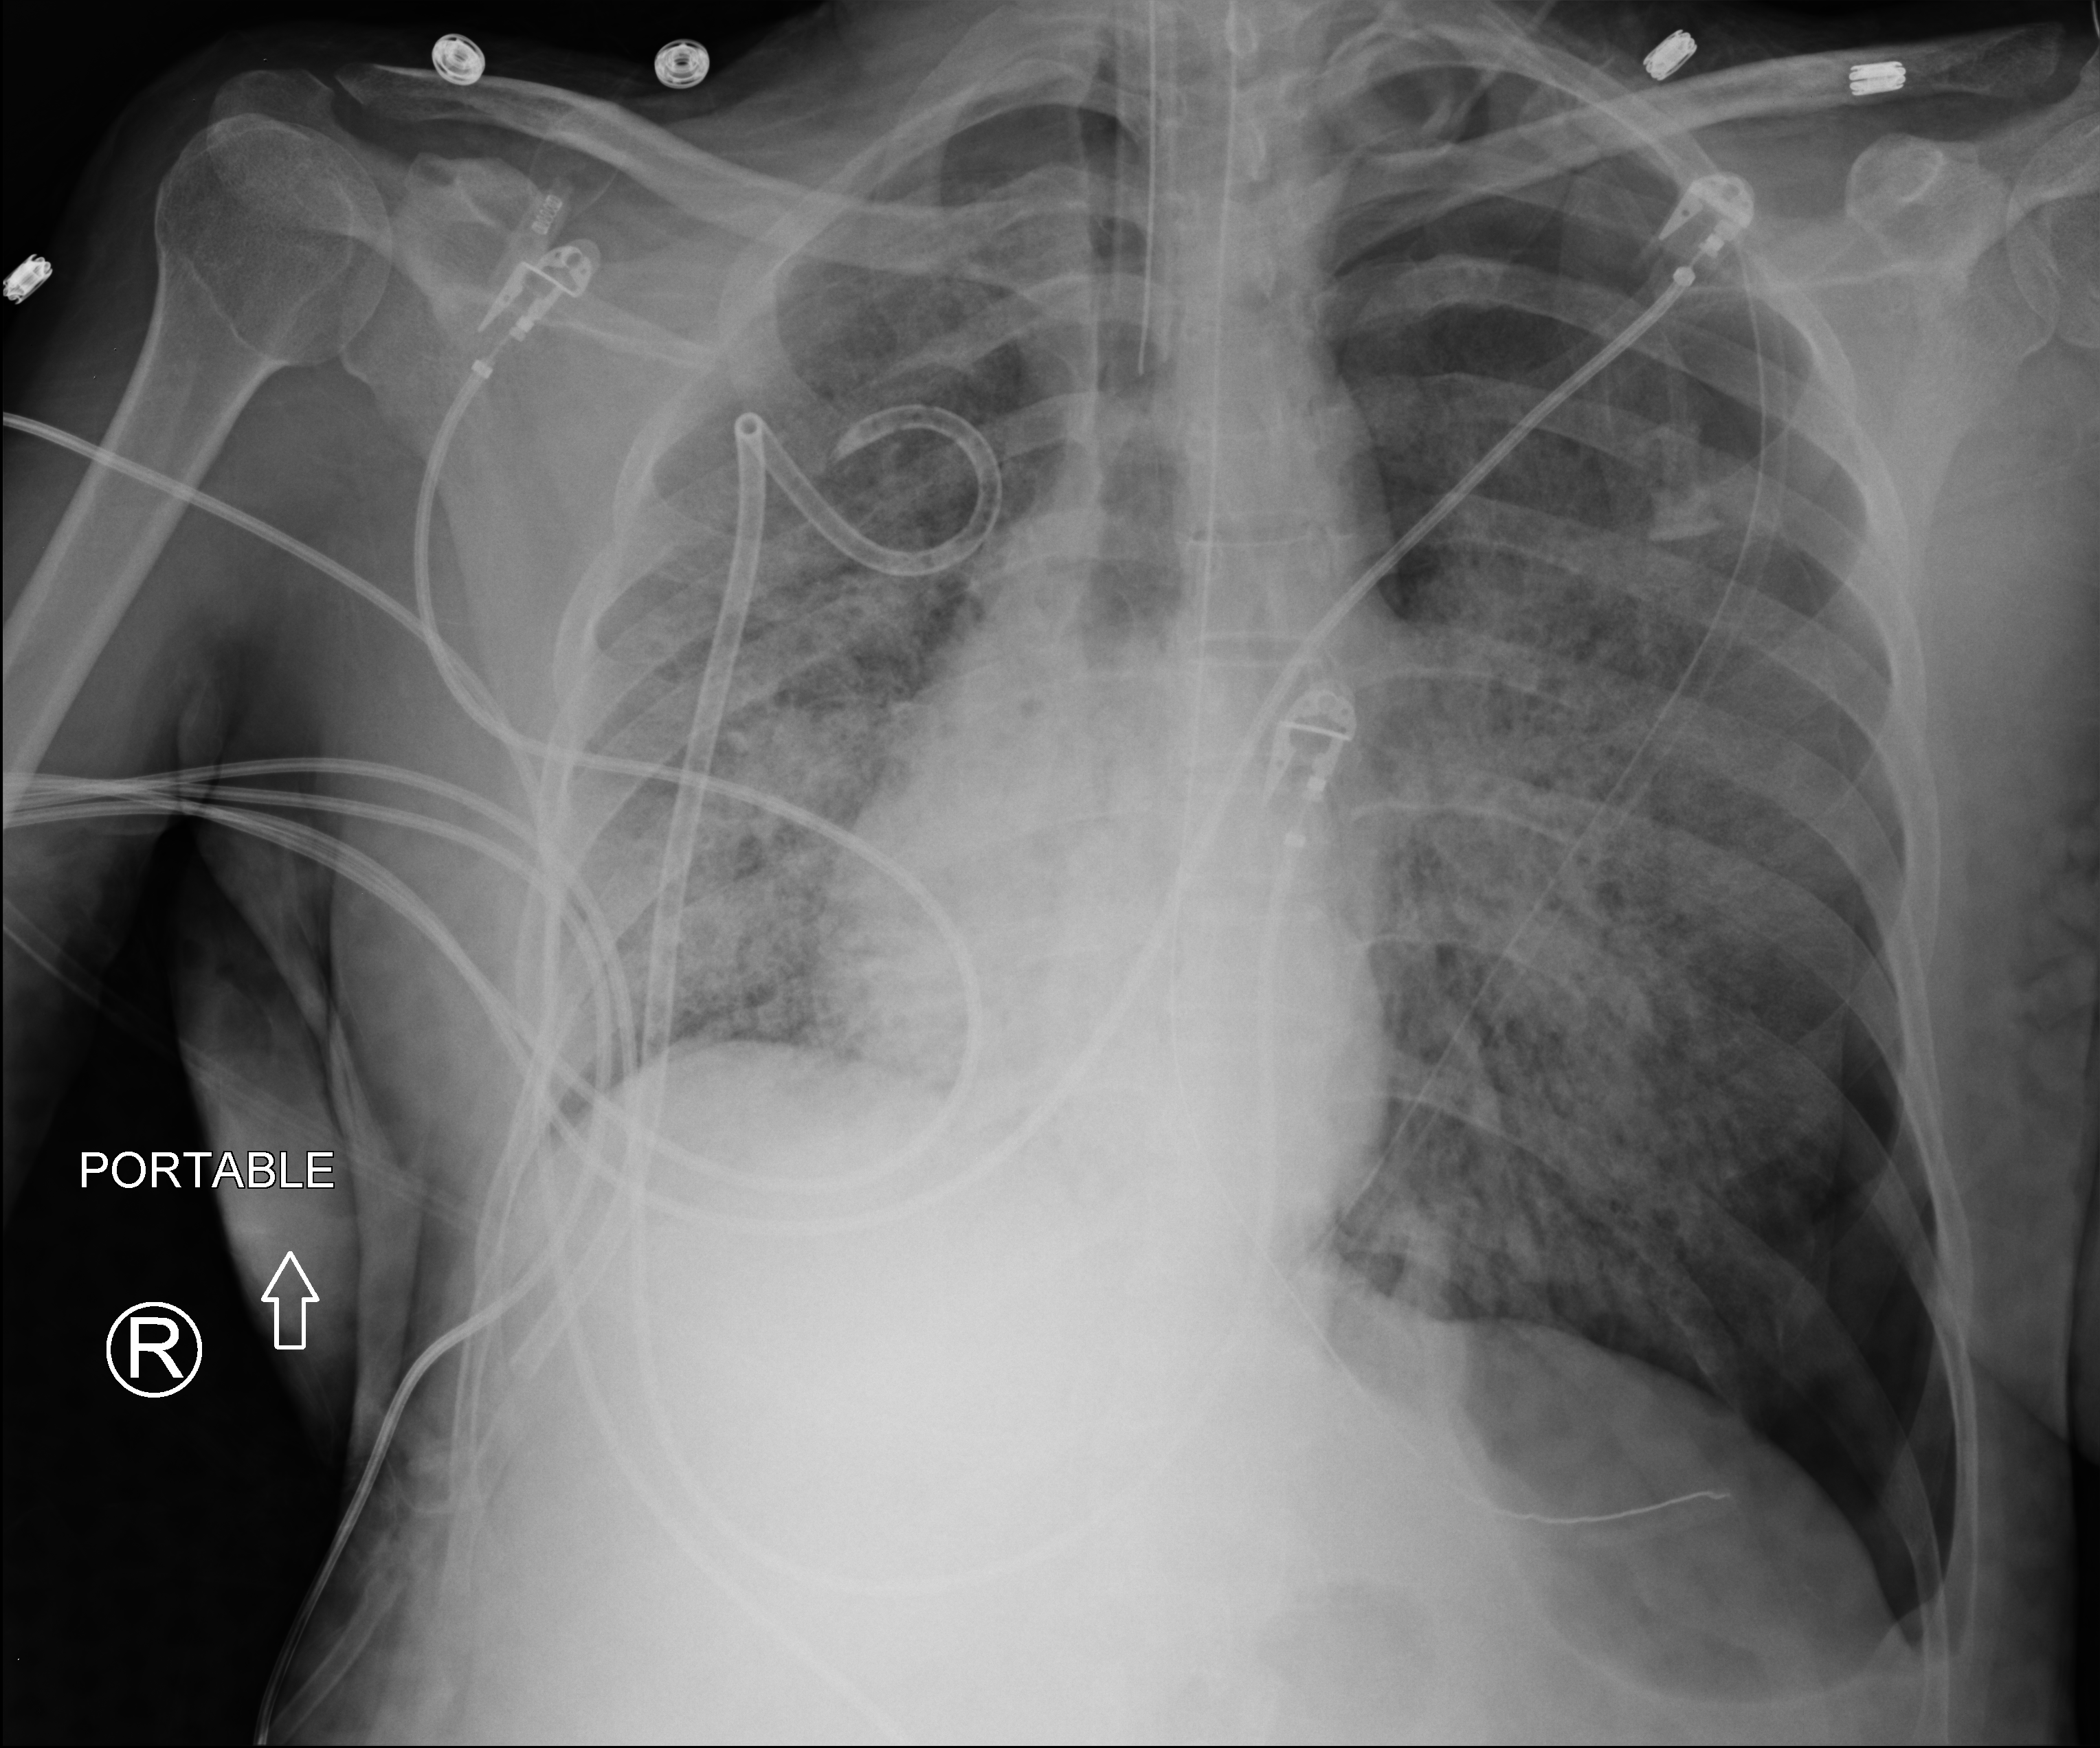
Chest X-ray (portable), anteroposterior (AP) projection. Patient hospitalised with COVID-19, aged 18–59 years.
From the hospital-stay record, not from the radiograph (when in the stay this image was taken is not recorded):
- mechanically ventilated during this hospital stay: yes